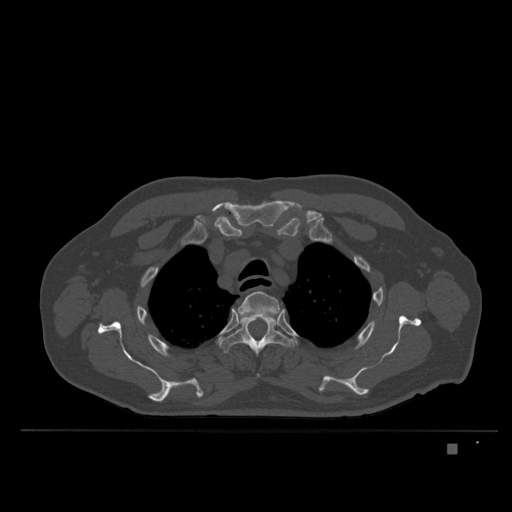
CT including the spine, one axial slice. Slice 292 of 435 in the series (ordered by position). Bone window (W 1800 / L 400 HU). 512 × 512 image matrix. Patient: male, 73 years. From the clinical record (not read from this slice): primary cancer: skin.
Annotated regions visible in this slice (semi-automatic segmentation, software-assisted and operator-edited):
- T3 vertebra: box from (x=237, y=291) to (x=281, y=319) px
- T4 vertebra: (x=219, y=317)–(x=295, y=355)